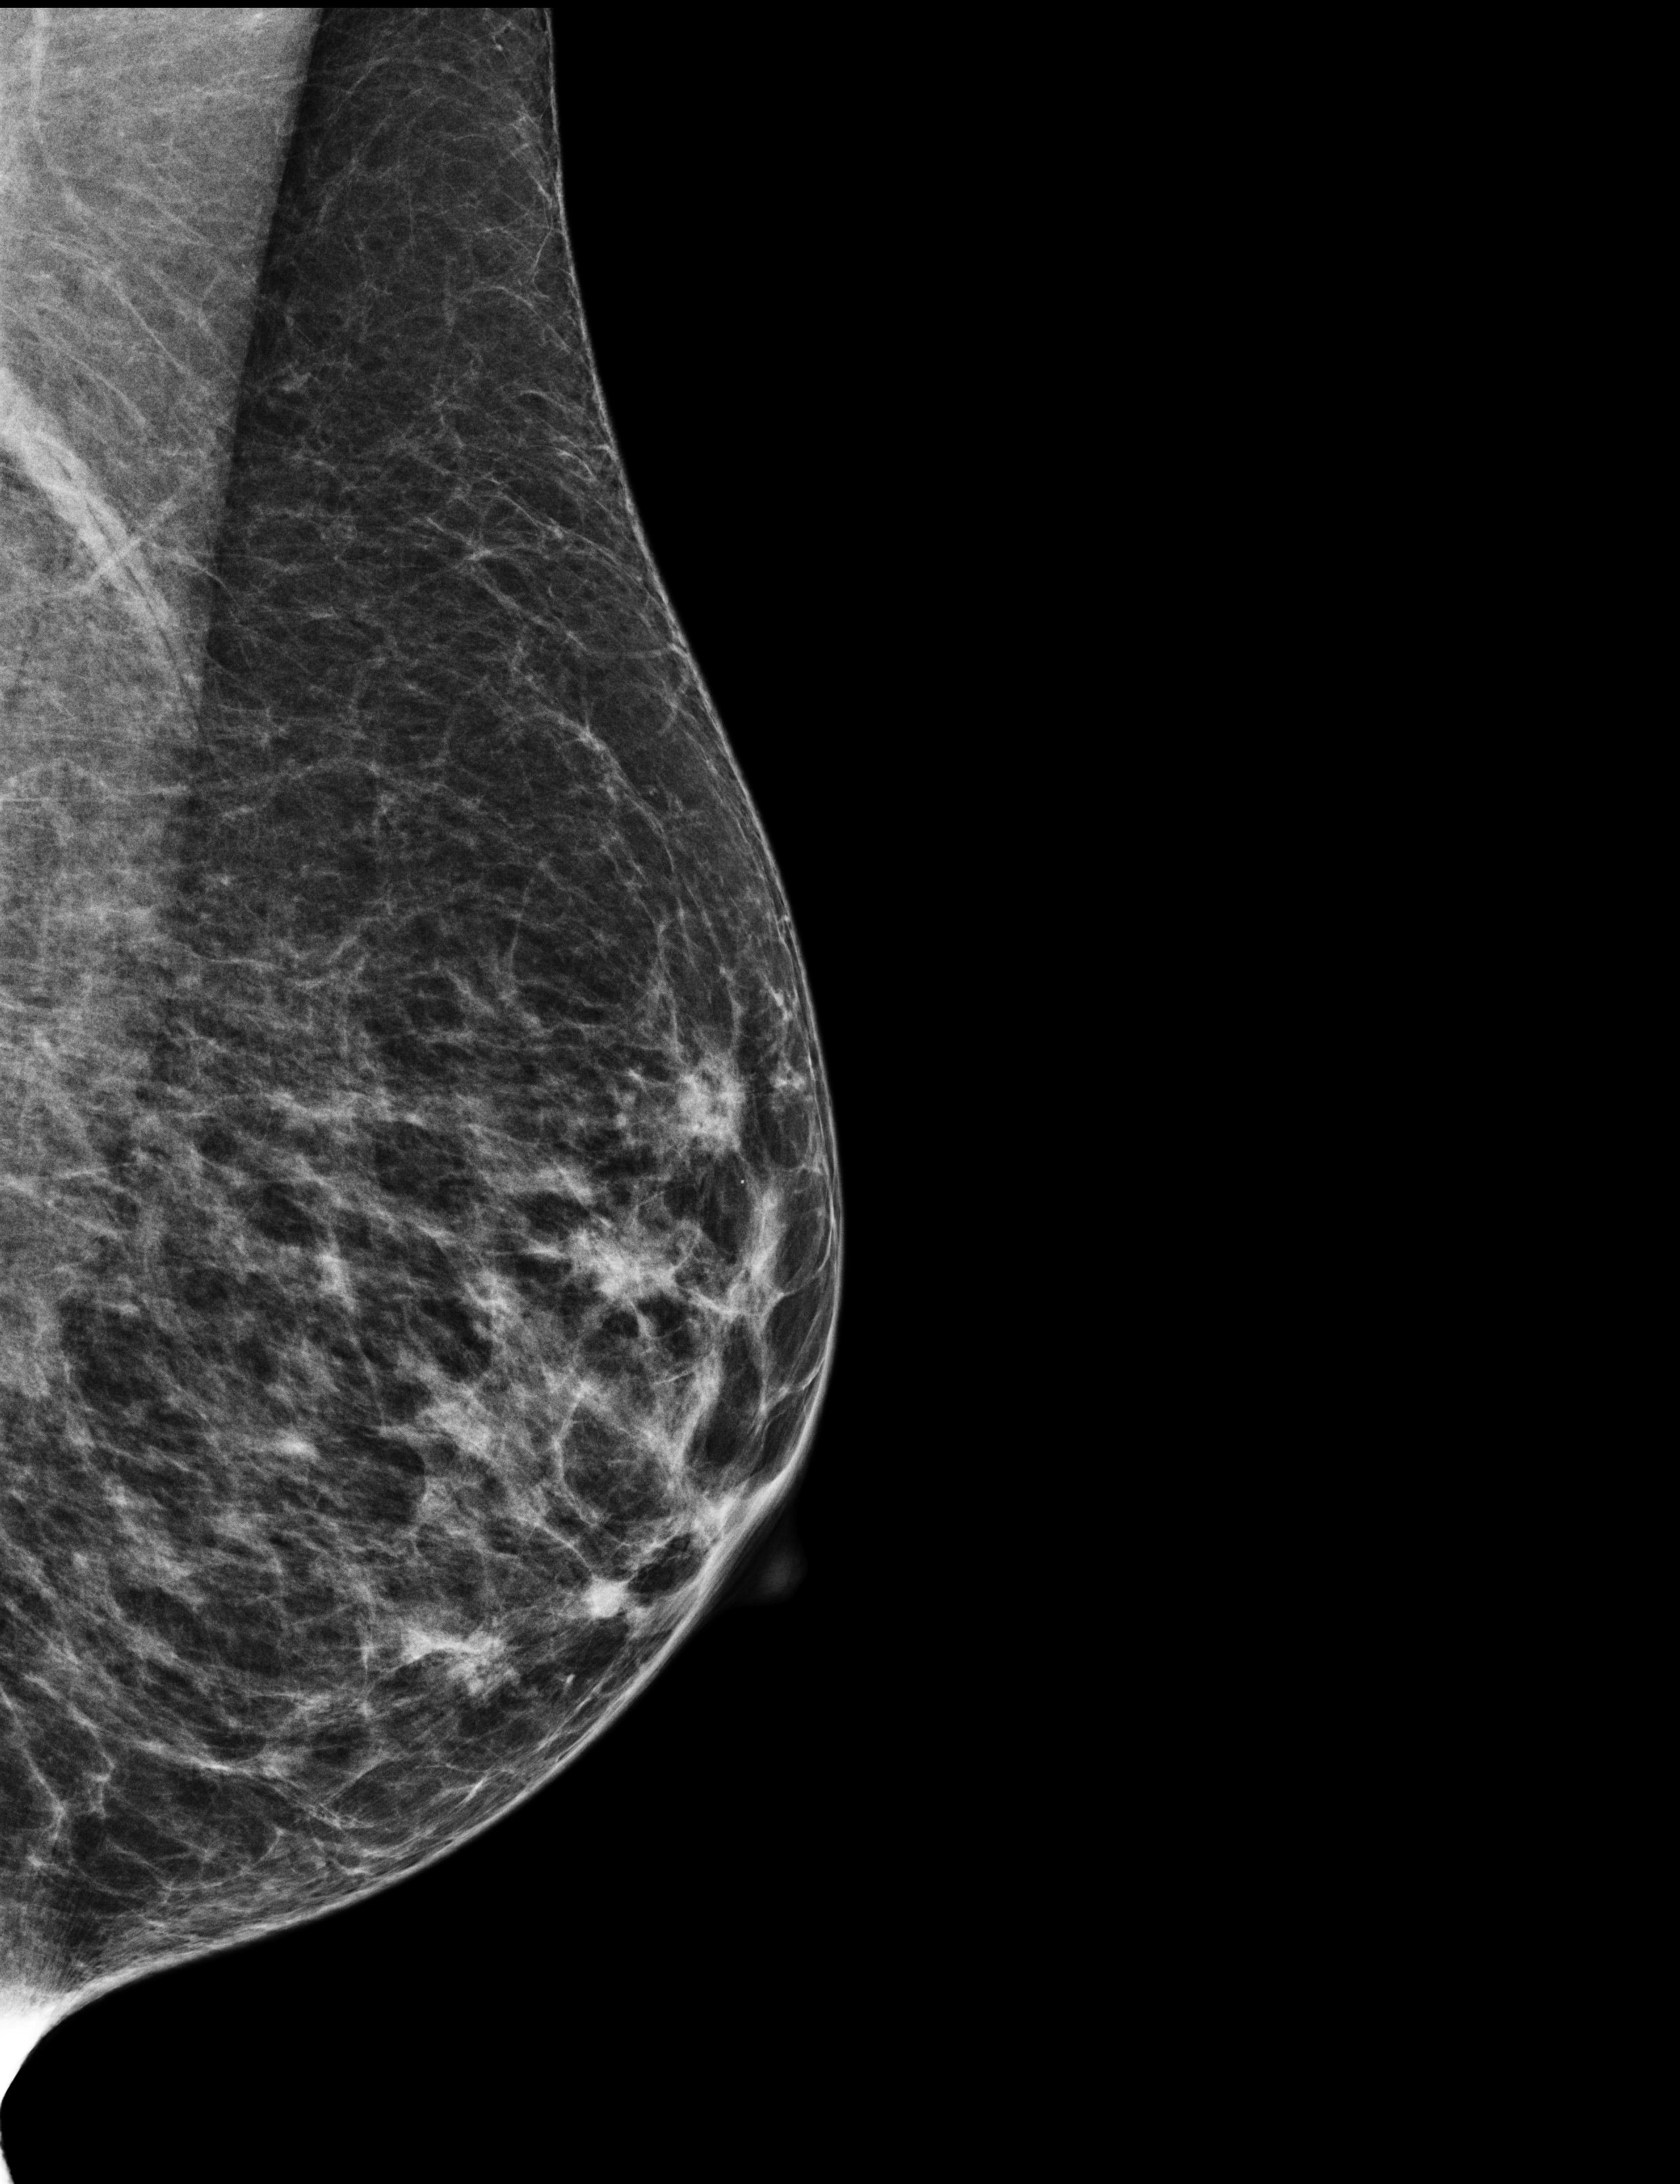
Annual screening mammography examination, compressed breast thickness 35 mm. Female patient, age 69 years.
Image type: full-field digital mammogram. Breast: left. Projection: mediolateral oblique (MLO) view. BI-RADS breast density category at the screening exam (both breasts, scale 1–4): 2. Final BI-RADS assessment for this screening round (tomosynthesis exam, both breasts): category 1. Recall: no recall after this screen.